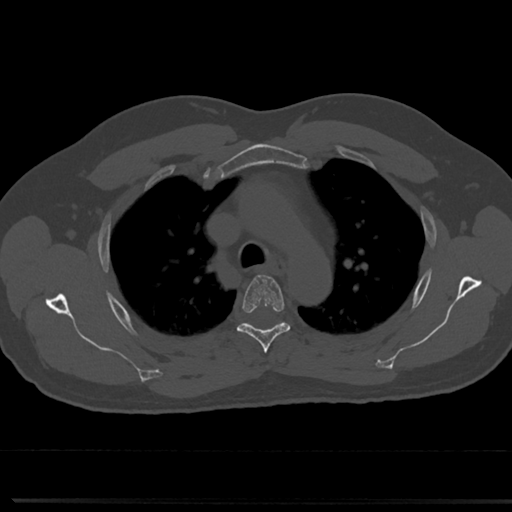
CT including the spine, one axial slice; position 542 of 817 along the scan axis; bone window (W 1800 / L 400 HU); 0.5 mm slice thickness; 512 × 512 image matrix, field of view 355 × 355 mm. Patient: male, 61 years. From the clinical record (not read from this slice): primary cancer: prostate.
Annotated regions visible in this slice (semi-automatic segmentation, software-assisted and operator-edited):
- T4 vertebra: box from (x=236, y=275) to (x=292, y=351) px
- T5 vertebra: (x=278, y=322)–(x=280, y=324)